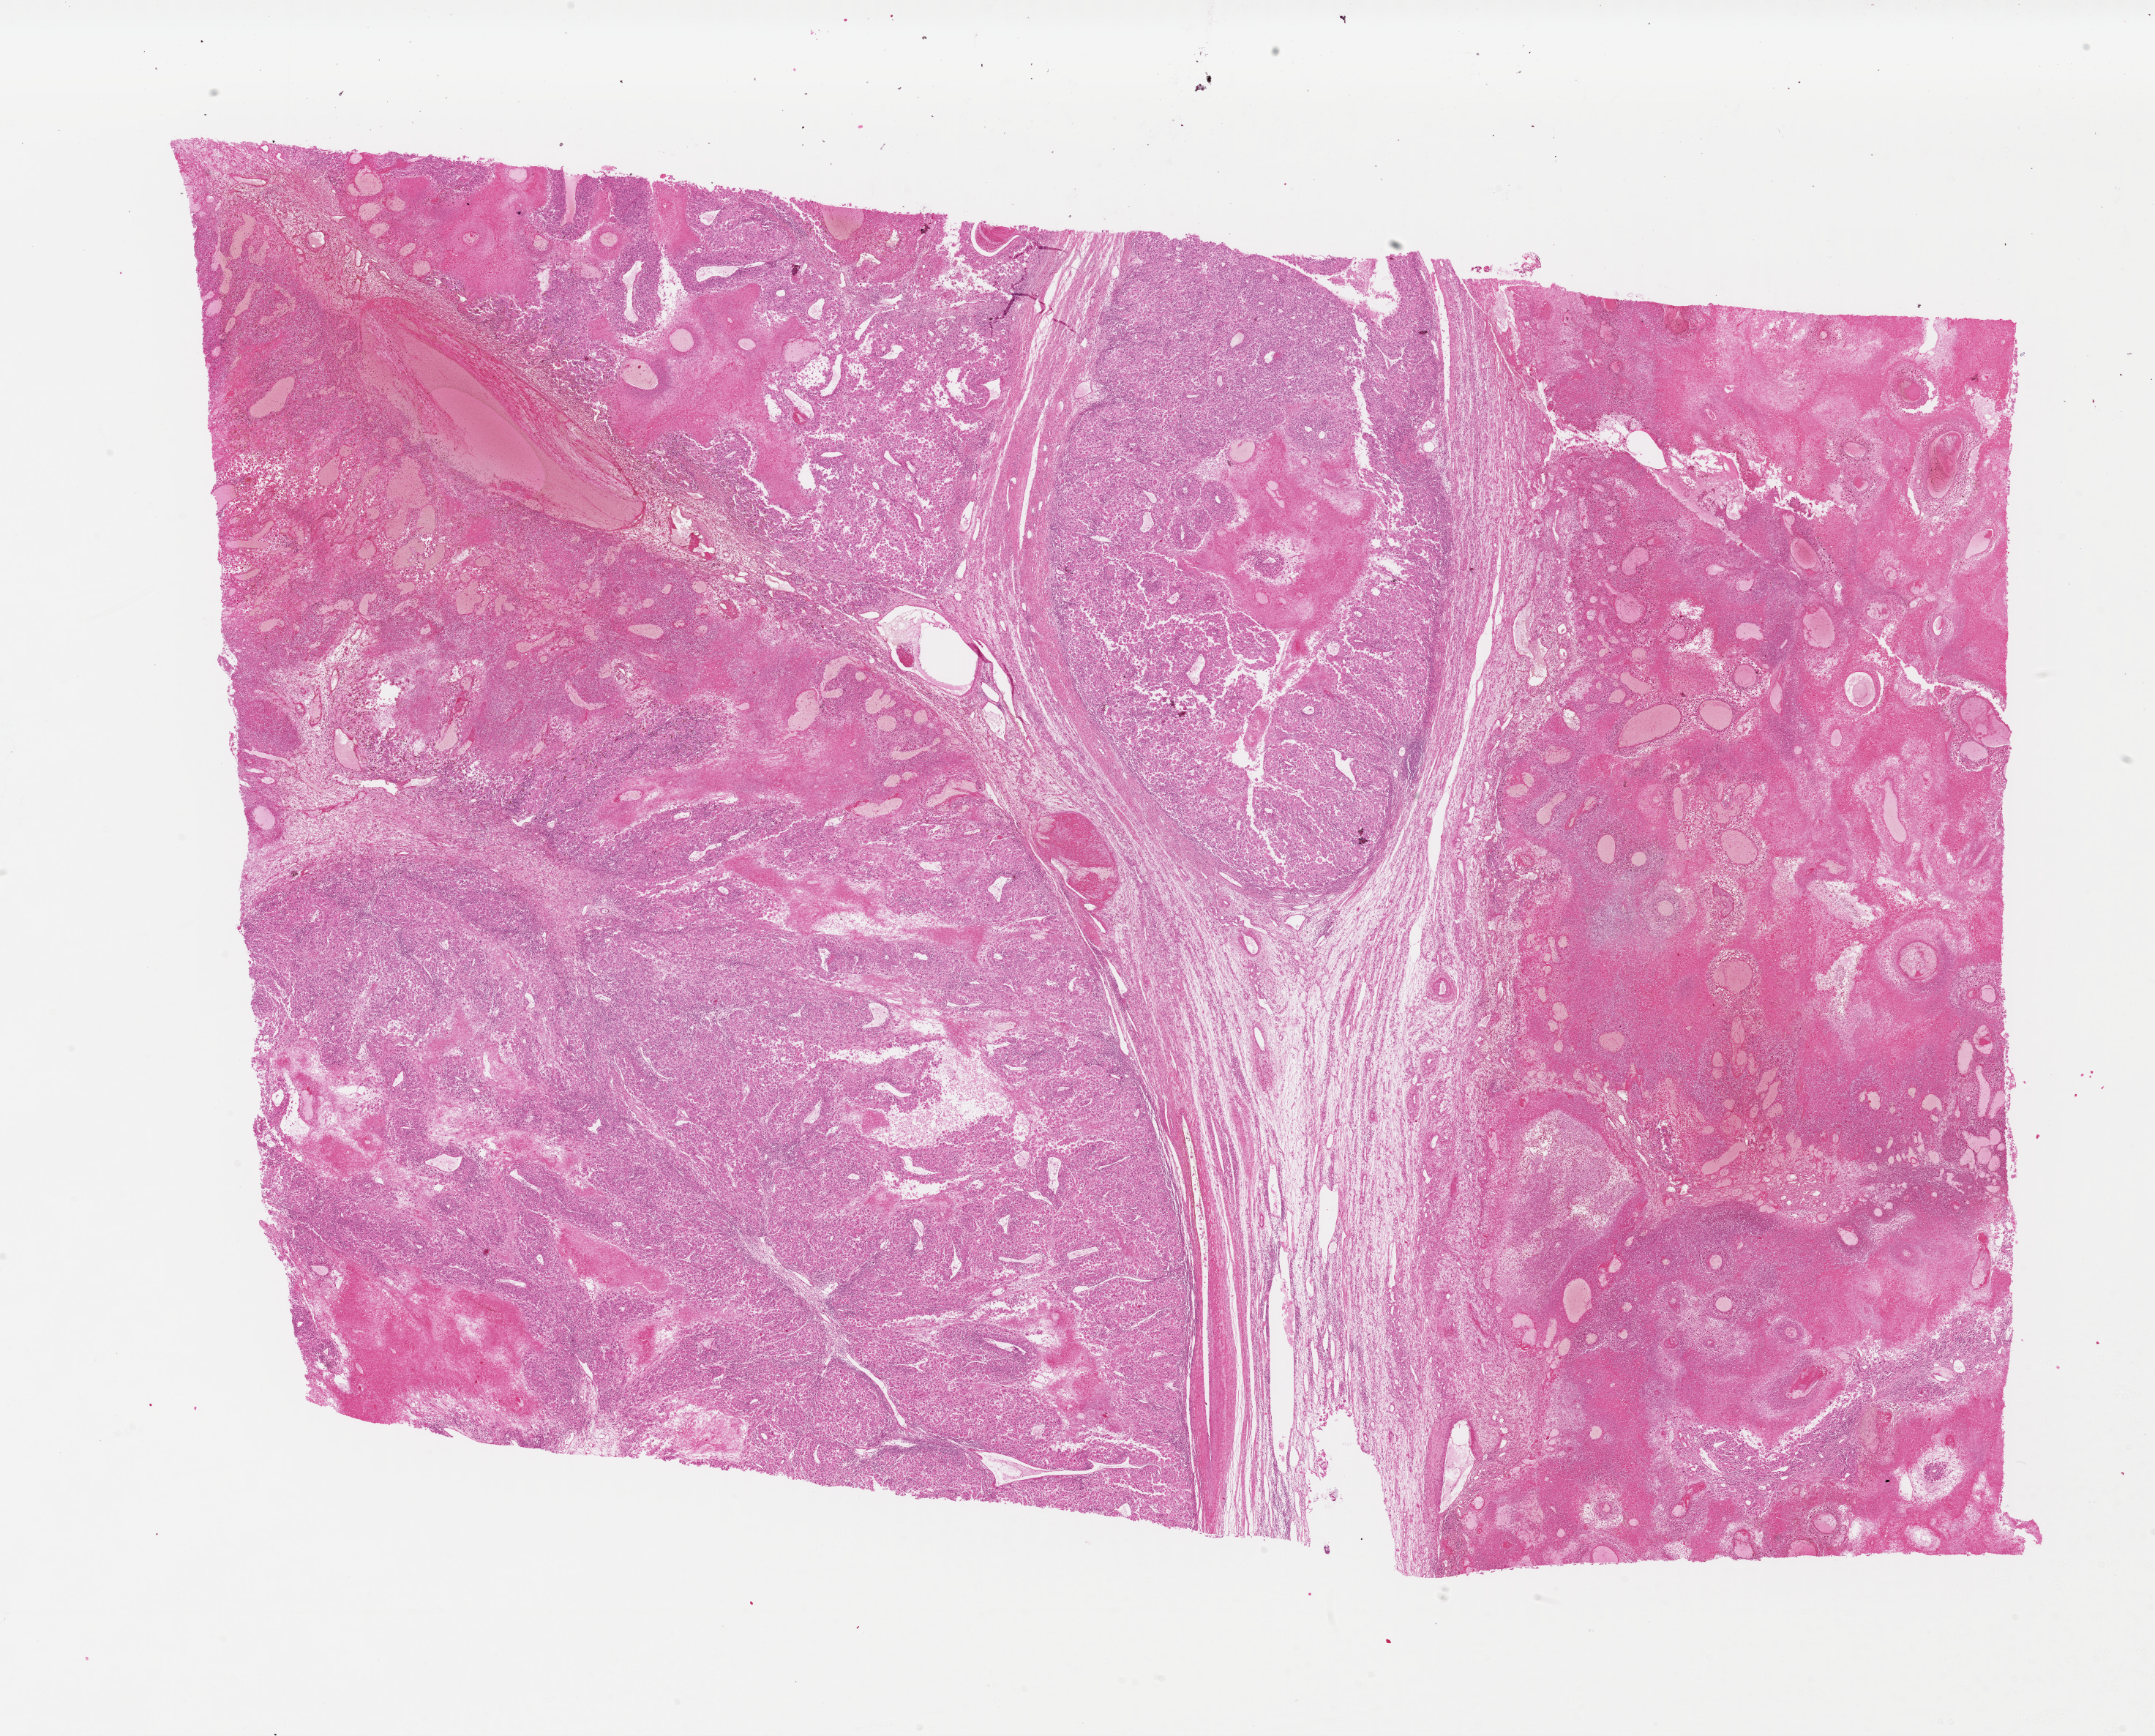
H&E whole-slide image — whole scanned area (about 23.1 x 18.6 mm, acquisition: 40x scan) shown as a low-resolution overview, formalin-fixed paraffin-embedded (FFPE) diagnostic section, skin, primary tumour sample. Female patient; age at initial diagnosis 18 years.
• pathologic diagnosis: Malignant melanoma, NOS